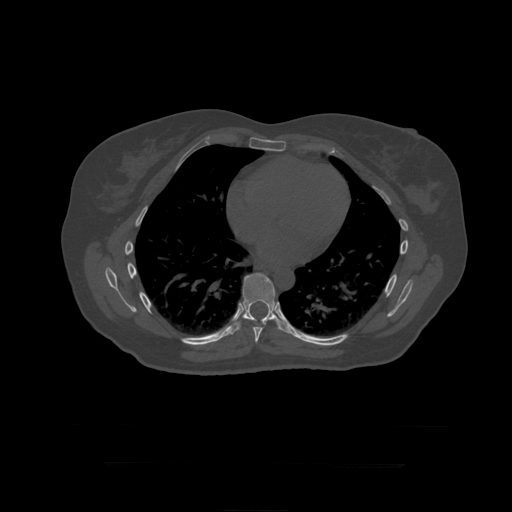
CT including the spine, one axial slice; slice 270 of 399 in the series (ordered by position); 120 kVp; bone window (W 1800 / L 400 HU); 1.25 mm slice thickness; 512 × 512 image matrix, field of view 450 × 450 mm. Patient age 41 years. Case-level facts recorded for this patient, not image findings: primary cancer: breast.
Outlined on this slice (semi-automatic segmentation, software-assisted and operator-edited):
- T8 vertebra: bounding box <253,327,264,343> (left, top, right, bottom; pixels)
- T9 vertebra: <228,273,290,336>